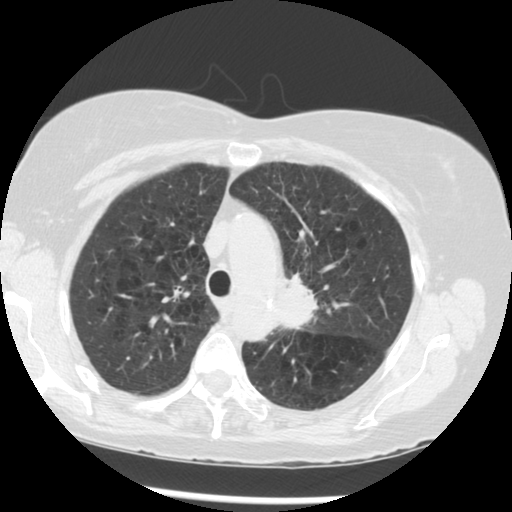
Low-dose screening chest CT, one axial slice. Position 211 of 283 along the scan axis. 120 kVp. Lung window (W 1500 / L -600 HU). 2.5 mm slice thickness. 512 × 512 image matrix.
Annotated regions visible in this slice (manually delineated by an expert):
- lesion 1 (tumor, upper lobe of left lung): box from (x=279, y=274) to (x=317, y=329) px